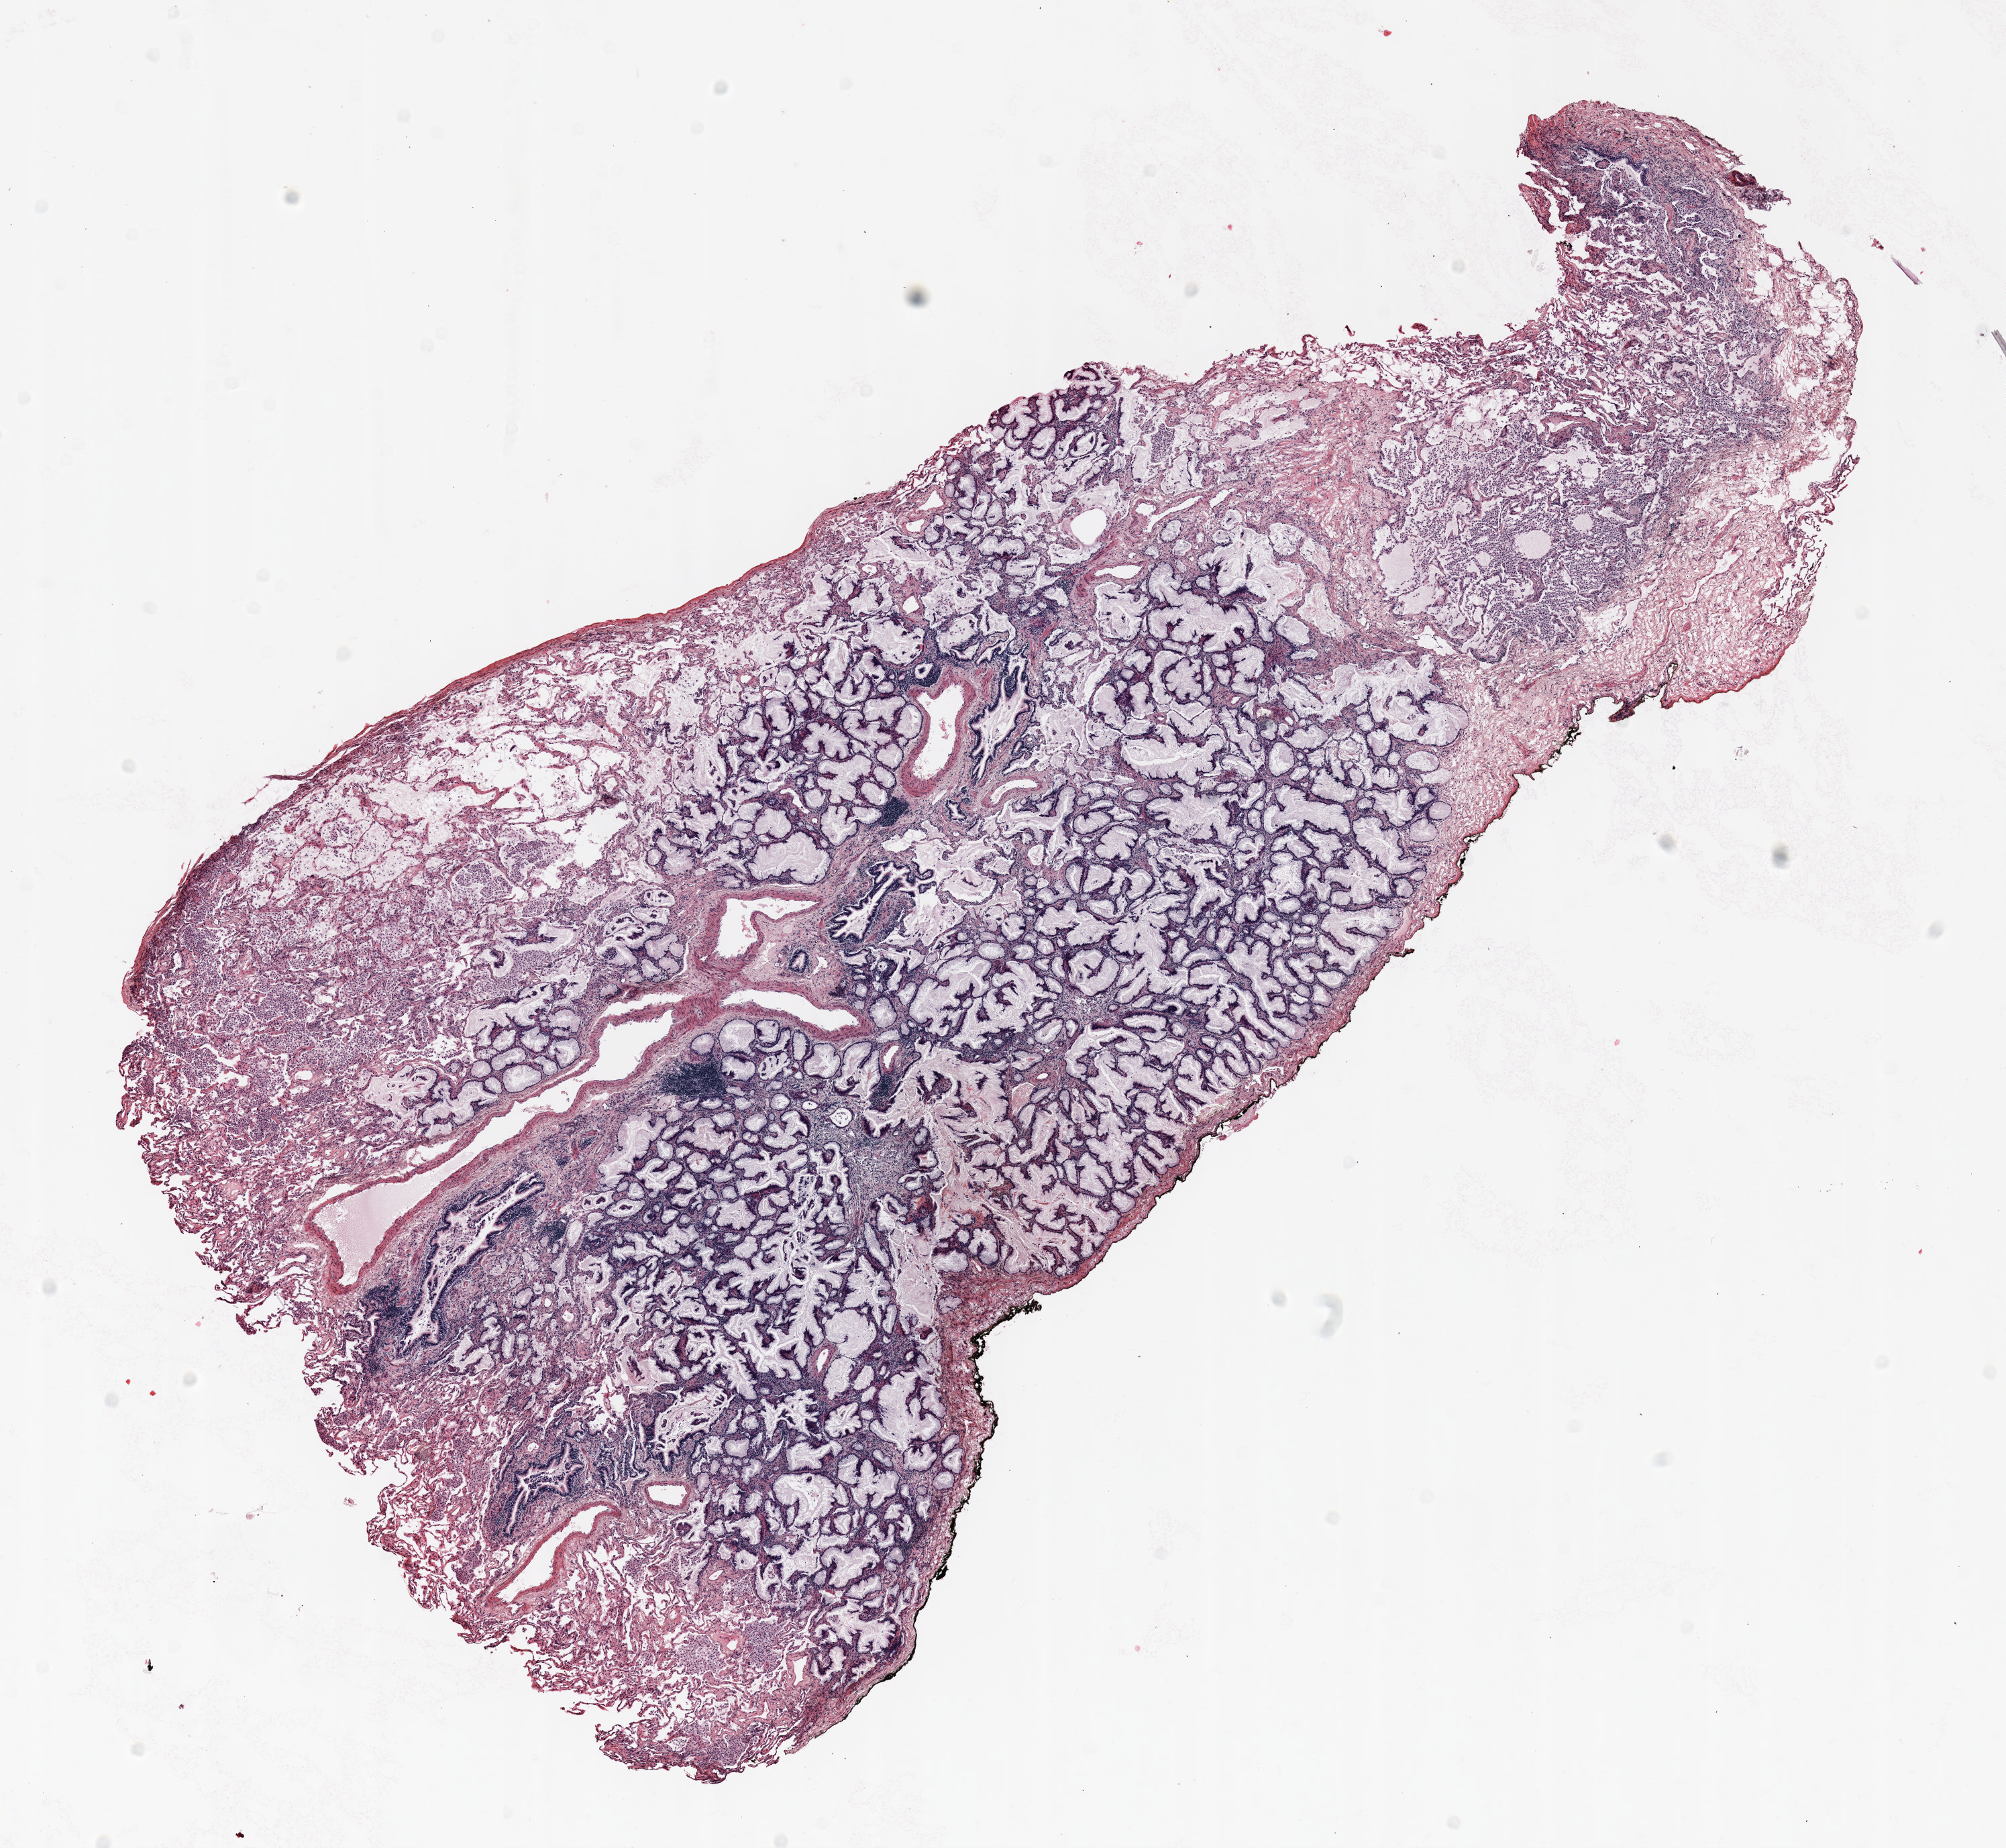
H&E whole-slide image, whole scanned area (about 12.0 x 11.1 mm) shown as a low-resolution overview. FFPE section. Lung. Female patient, aged 64 at enrolment. Former smoker at enrolment. Grade: well differentiated (G1).
- ICD-O-3 topography: lower lobe of lung (C34.3)
- tumour size (pathology): 8 mm
- primary tumour location (clinical record): left lower lobe
- participant's lung-cancer diagnosis: Bronchiolo-alveolar adenocarcinoma, NOS
- stage (AJCC 6th edition): IA